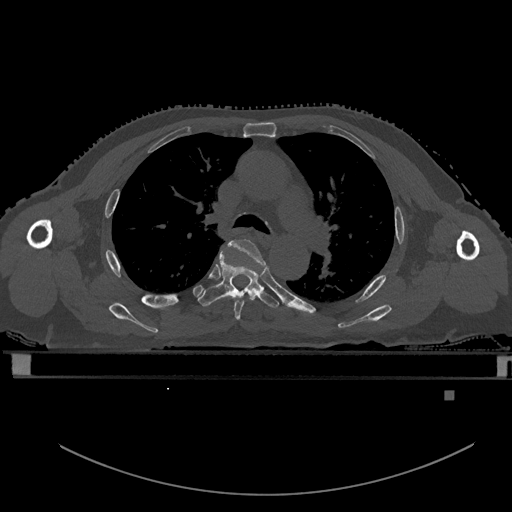
CT including the spine, one axial slice; position 376 of 969 along the scan axis; bone window (W 1800 / L 400 HU); 0.5 mm slice thickness; 512 × 512 image matrix, field of view 456 × 456 mm. Male patient, age 82 years. From the clinical record (not read from this slice): primary cancer: prostate; vertebrae with lytic lesions (as recorded): T11, T9, T8, T2.
Outlined on this slice (semi-automatic segmentation, software-assisted and operator-edited):
- T4 vertebra: bounding box <223,239,265,320> (left, top, right, bottom; pixels)
- T5 vertebra: <198,252,279,308>